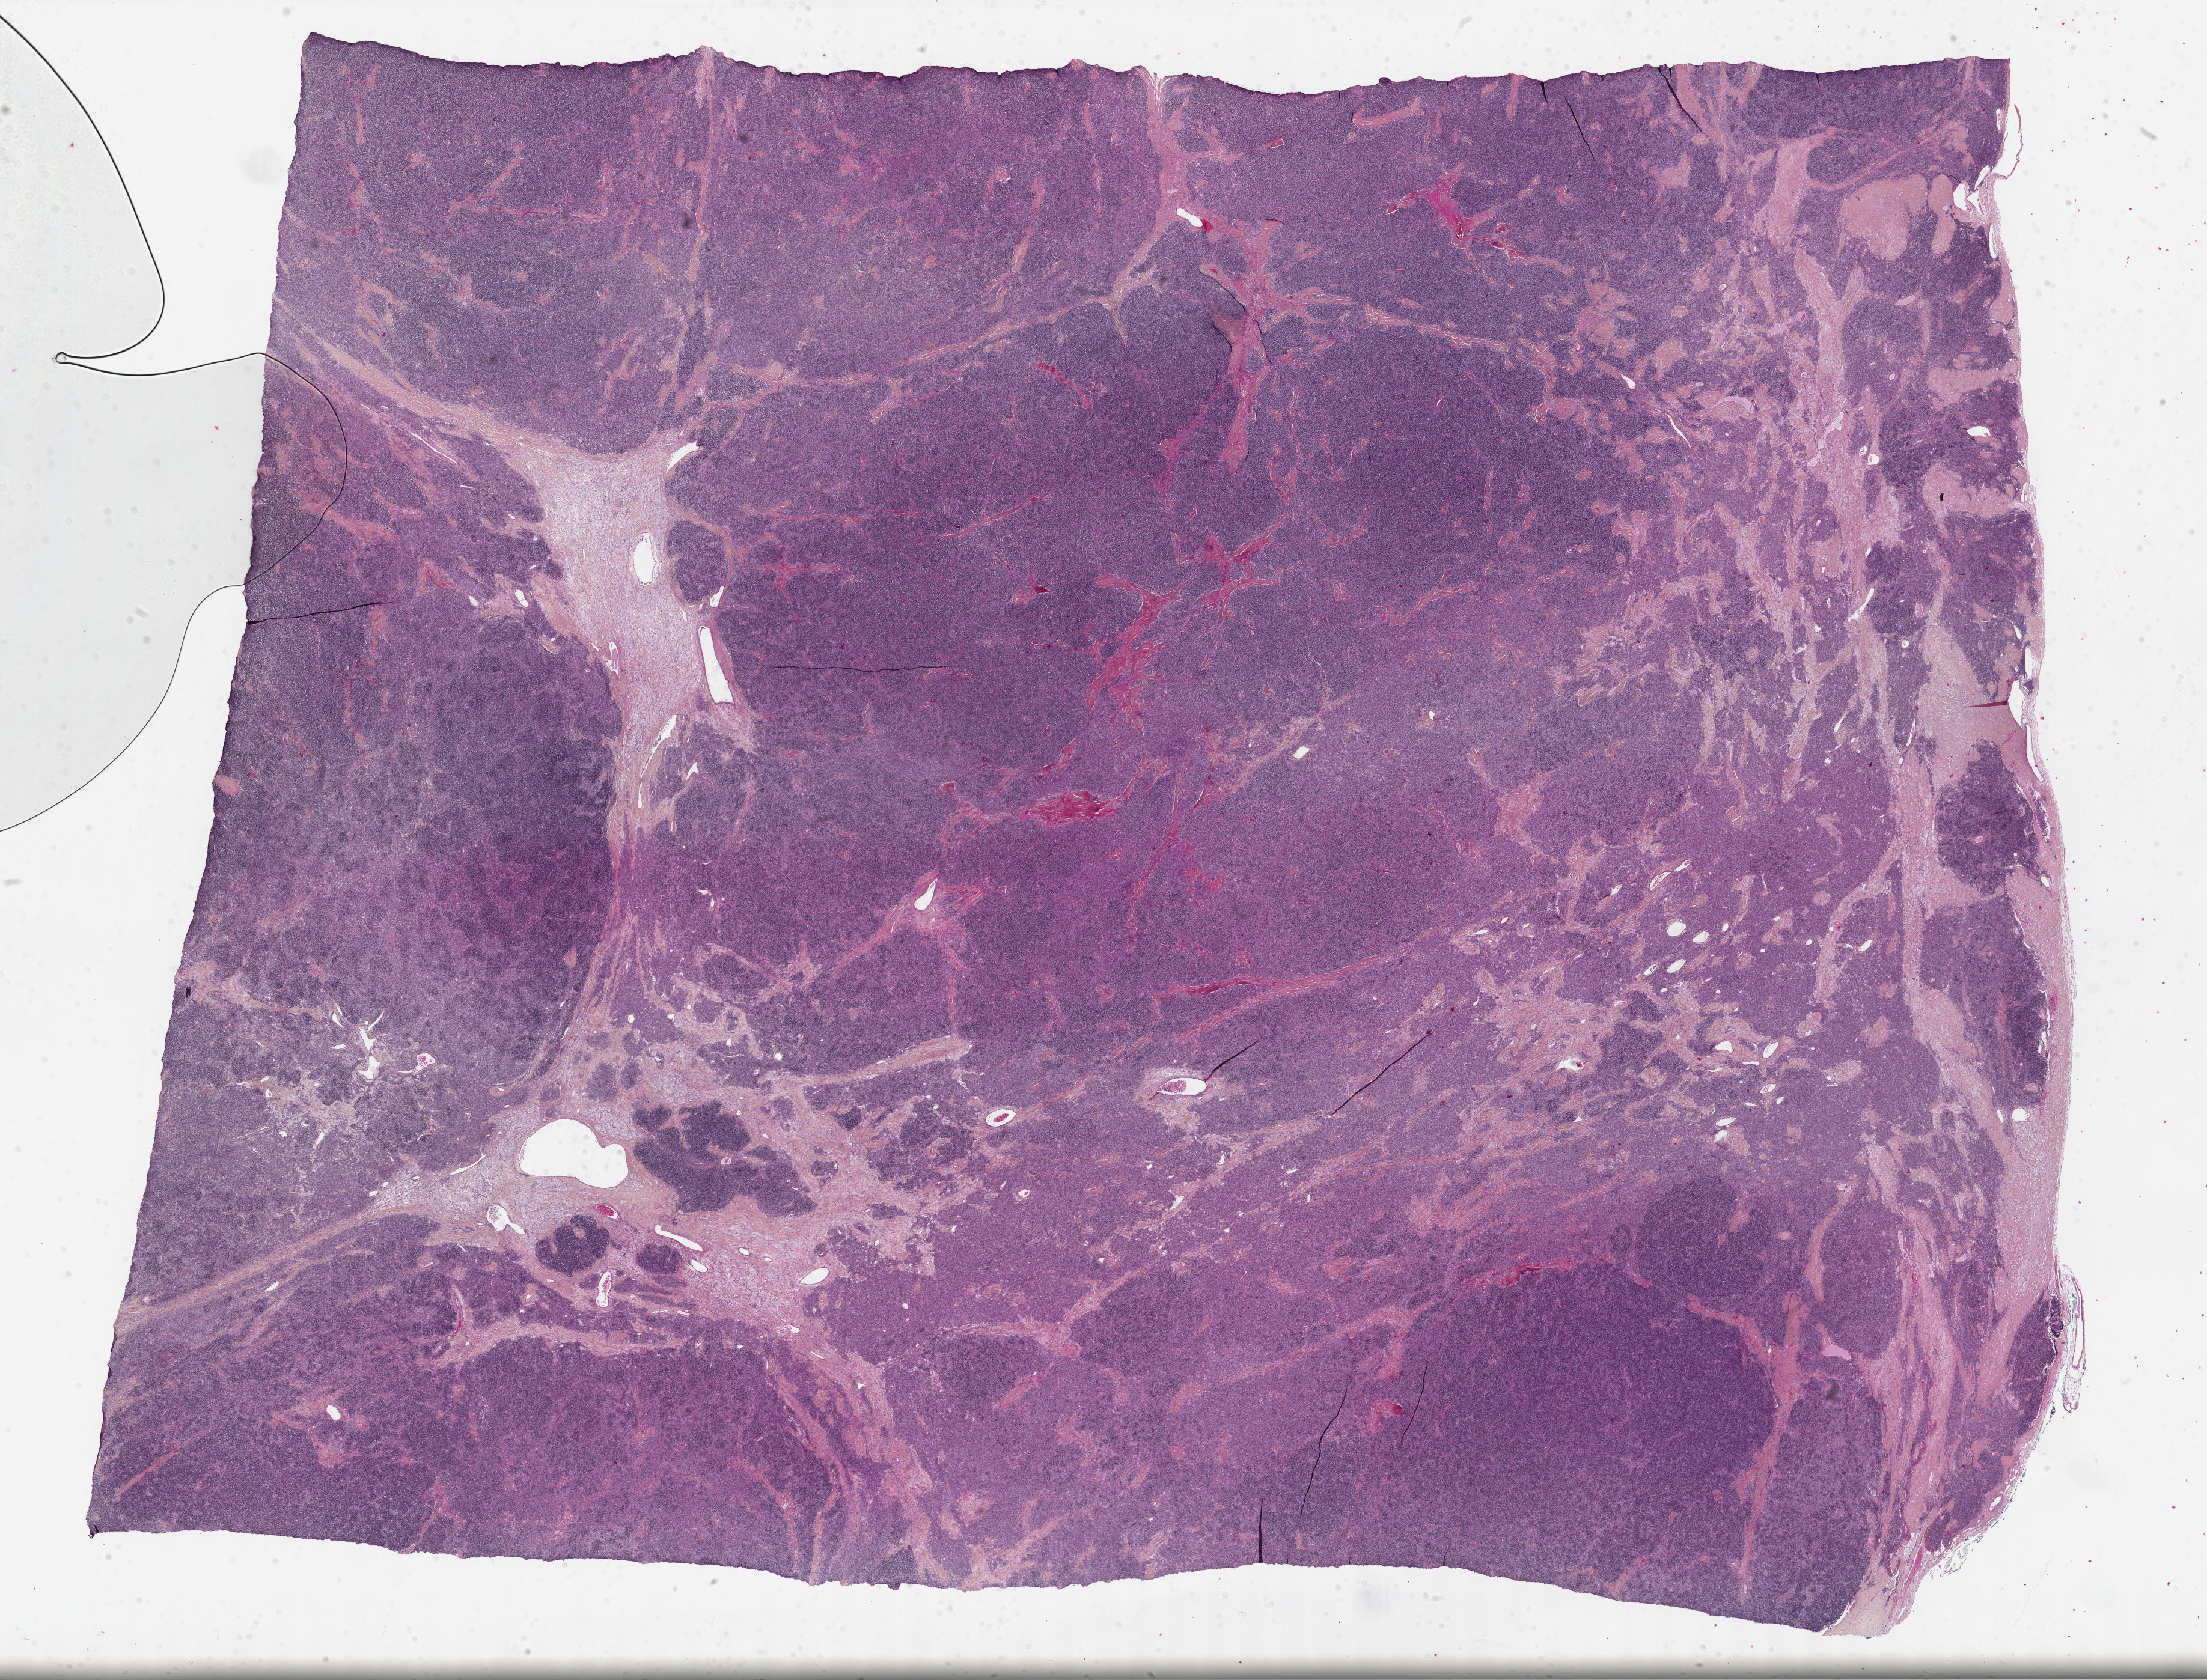
Whole-slide histology image, H&E-stained — a low-resolution overview of the entire scanned area, about 29.7 x 22.6 mm, FFPE section, primary tumour sample from the thymus. Patient: female, age at initial diagnosis 77 years.
Pathologic diagnosis: Thymoma, type AB, malignant.